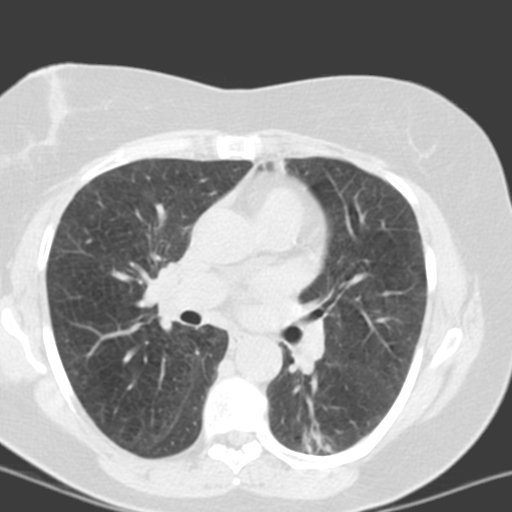
Axial slice from a low-dose chest CT screening exam. Third screening round (two years after baseline). Lung window (W 1500 / L -600 HU). Slice 60 of 150 in the series. Female participant, aged 55 years at enrolment.
Lesion marked by an expert reader, box from (x=287, y=412) to (x=365, y=464) px. The screening reader recorded 6 non-calcified nodules or masses ≥4 mm on this exam (left lower lobe, left lower lobe, left upper lobe, lingula, lingula, right middle lobe); which of them this box marks is not recorded.